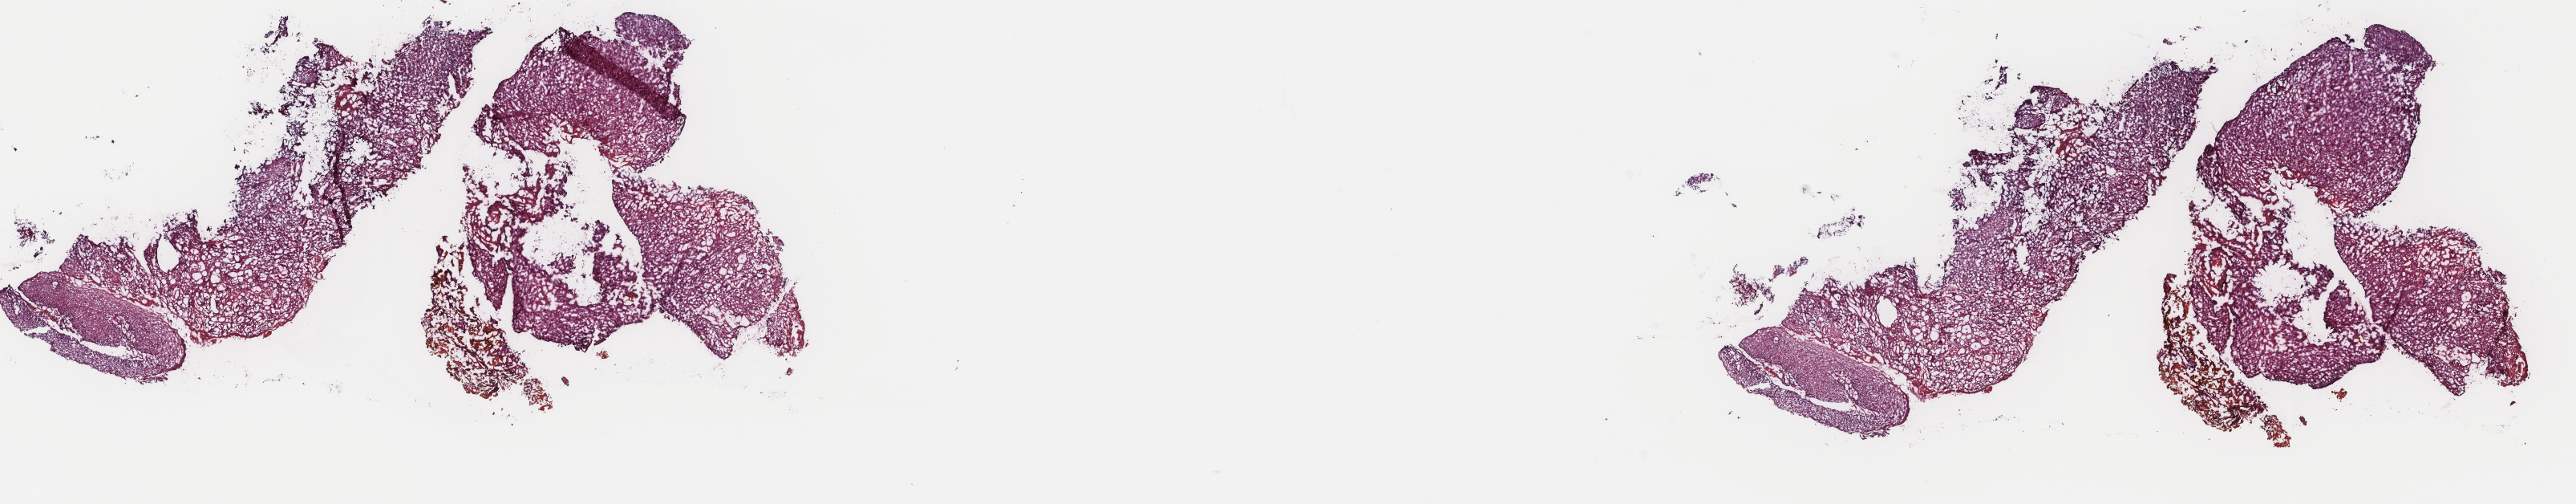
Digitized H&E tissue section (whole slide), low-resolution overview of the scanned area, about 25.5 x 5.0 mm. Frozen section. Sample: primary tumour, head and neck. Male, age 71 years at initial diagnosis. Histologic grade: G3 (poorly differentiated). Slide review estimates, as recorded: tumour cells 100%, tumour nuclei 75%, normal cells 0%, stromal cells 0%, necrosis 0%. Inflammatory infiltration, as recorded: lymphocyte infiltration 4%, monocyte infiltration 0%, neutrophil infiltration 0%.
AJCC pathologic stage: III (7th edition). Lymph nodes positive (case pathology): 1 of 40 examined. Histologic diagnosis: Squamous cell carcinoma, NOS (floor of mouth, NOS).